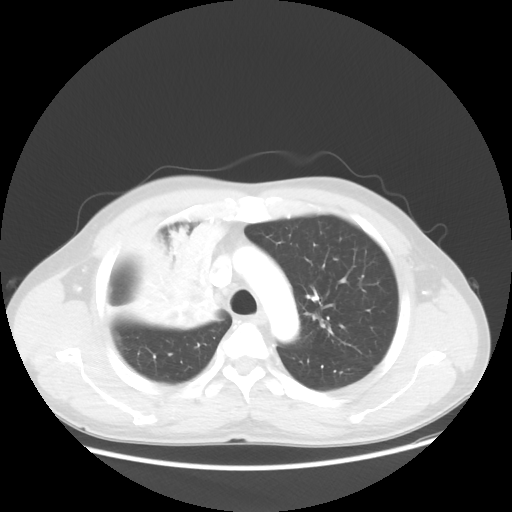
Chest CT, one axial slice; slice 40 of 56 in the series (ordered by position); reconstruction kernel STANDARD; lung window (W 1500 / L -600 HU); 5 mm slice thickness; 512 × 512 image matrix. Patient: male, 60 years. Case-level facts recorded for this patient, not image findings: clinical TNM (as recorded): T2a N1 M0.
Annotated regions visible in this slice (bounding box drawn by a radiologist):
- lung tumour (recorded histology: squamous cell carcinoma): bounding box (x1, y1, x2, y2) in pixels: (137, 218, 234, 333)